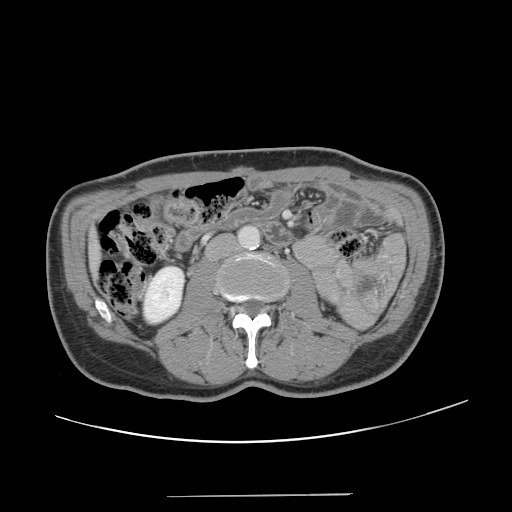
Contrast-enhanced abdominal CT, one axial slice; slice 38 of 131 in the series (ordered by position); 120 kVp; soft-tissue window (W 400 / L 40 HU); 2.5 mm slice thickness; 512 × 512 image matrix. Male patient, age 60 years. From the clinical record (not read from this slice): diagnosis: colorectal cancer liver metastases, imaged before liver resection; multiple liver metastases: no; largest metastasis: 2.5 cm; disease in both lobes: no.
Outlined on this slice (manually delineated by an expert):
- liver: bounding box <94,246,97,268> (left, top, right, bottom; pixels)
- planned liver remnant (the part of the liver to remain after resection): <94,242,96,263>